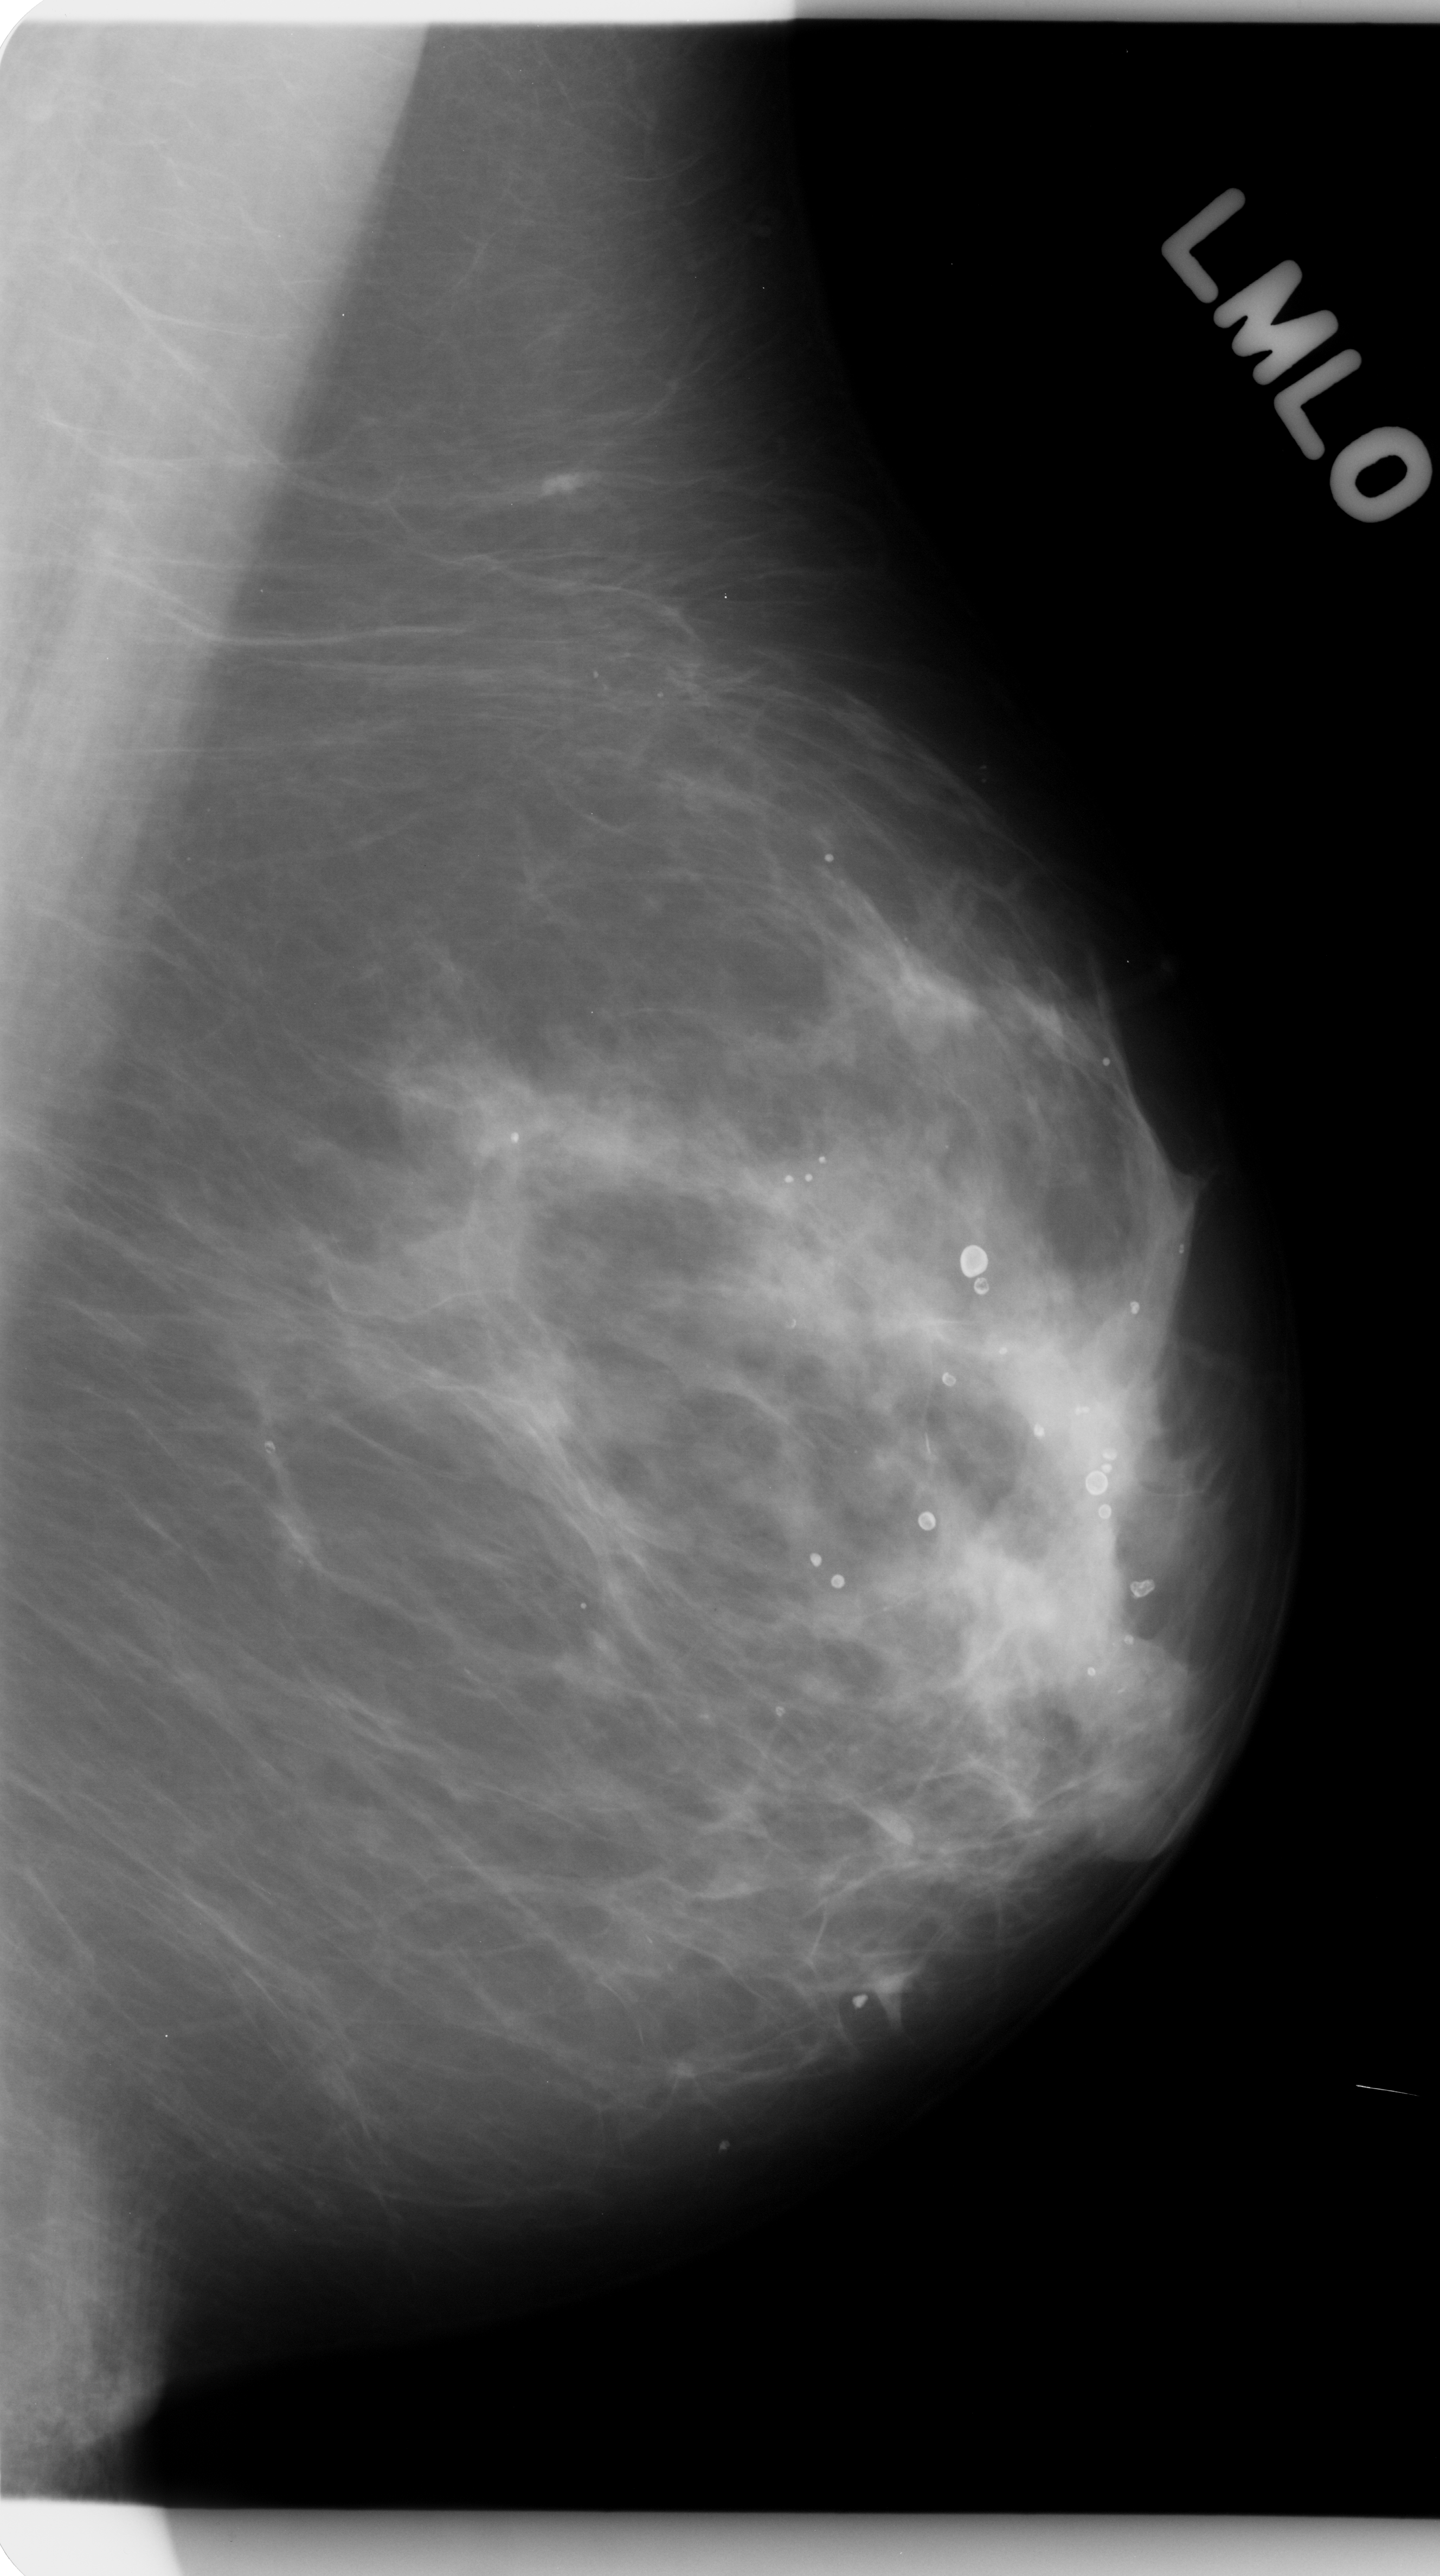
Digitized screen-film mammogram; left breast; mediolateral oblique (MLO) view; breast composition: scattered fibroglandular densities (BI-RADS density category 2 of 4).
Abnormality record for this image: mass, shape architectural distortion, margins spiculated; BI-RADS assessment category 4; pathology (as recorded): benign.